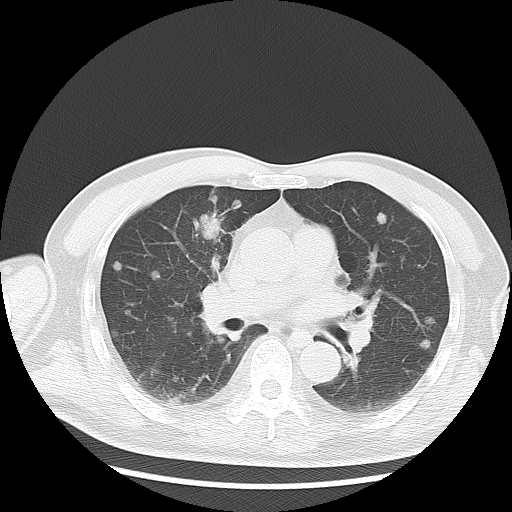
Chest CT, one axial slice; position 10 of 36 along the scan axis; reconstruction kernel LUNG; 120 kVp; lung window (W 1500 / L -600 HU); 5 mm slice thickness; 512 × 512 image matrix, field of view 369 × 369 mm. Male patient, age 57 years. From the clinical record (not read from this slice): clinical TNM (as recorded): T2 N3 M1a.
Structures marked on this image (bounding box drawn by a radiologist):
- lung tumour (recorded histology: adenocarcinoma): box from (x=193, y=209) to (x=228, y=246) px